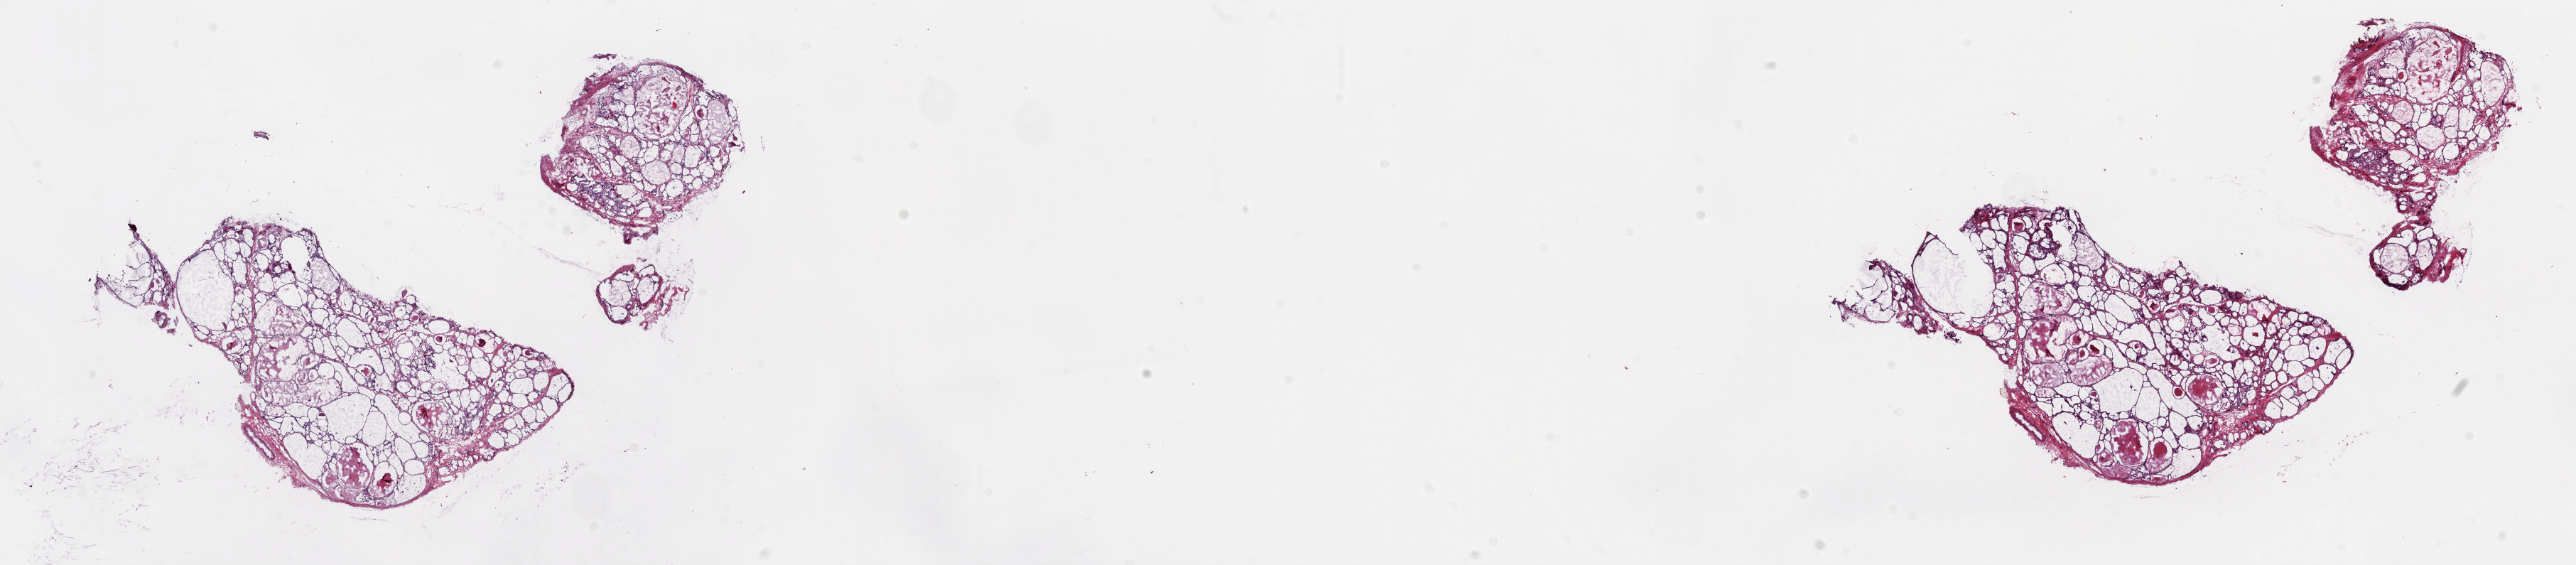
Whole-slide histology image, Hematoxylin and eosin (H&E) stained — low-resolution overview of the scanned area, about 28.8 x 6.3 mm. Frozen section from the top of the tissue portion. Thyroid, solid tissue normal (non-tumour tissue) sample. Female patient; age at initial diagnosis 72 years. Slide review estimates, as recorded: tumour cells 0%, tumour nuclei 0%, normal cells 100%, stromal cells 0%, necrosis 0%. Infiltration values recorded for this section: lymphocyte infiltration 0%, monocyte infiltration 0%, neutrophil infiltration 0%.
This section: solid tissue normal sample (biorepository sample class). Patient diagnosis: Papillary adenocarcinoma, NOS (thyroid gland).